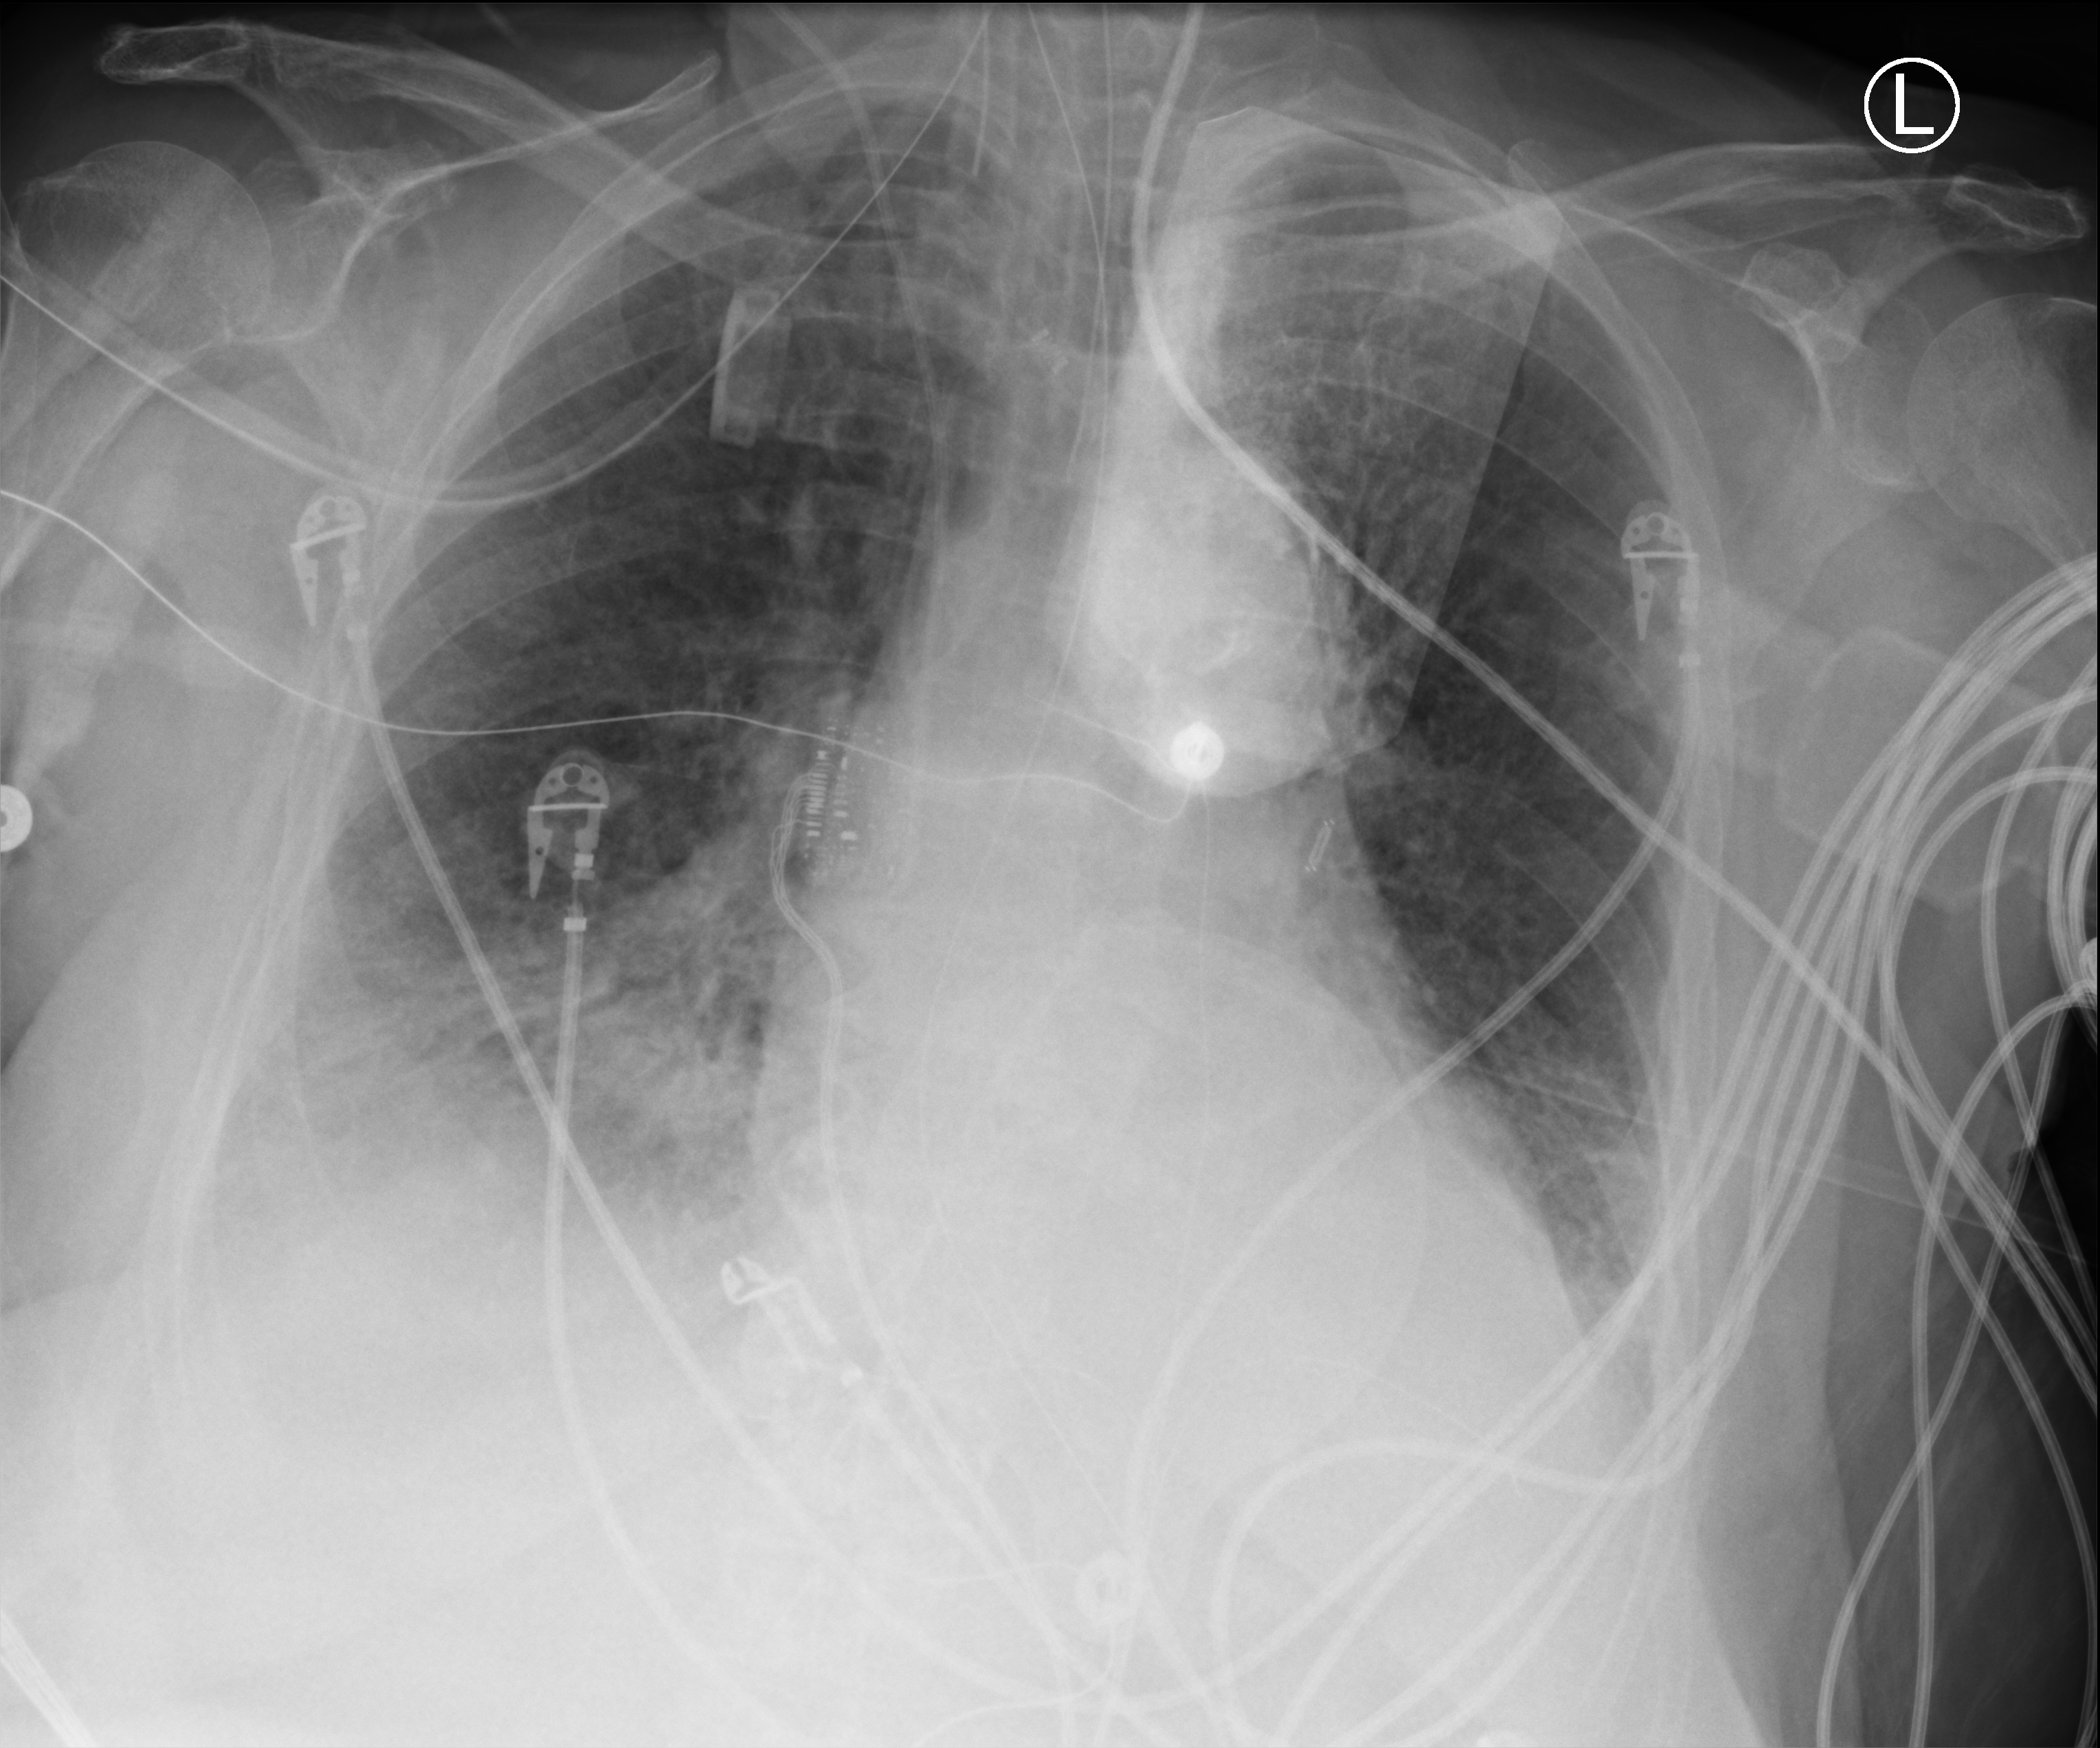
Chest X-ray (portable); anteroposterior (AP) projection. Patient hospitalised with COVID-19; female, aged 75–90 years.
From the hospital-stay record, not from the radiograph (when in the stay this image was taken is not recorded):
- hypertension (admission record): yes
- admitted to intensive care during this hospital stay: yes
- smoking status (admission record): former